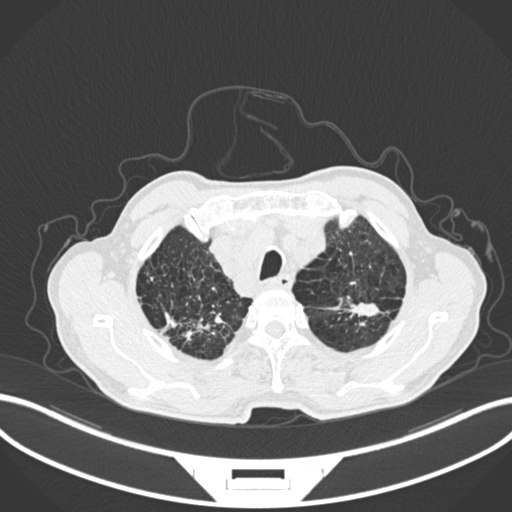
Chest CT, one axial slice. 120 kVp. Lung window (W 1500 / L -600 HU). 512 × 512 image matrix. Patient: male, 74 years. Case-level facts recorded for this patient, not image findings: clinical TNM (as recorded): T2a N1 M0.
Structures marked on this image (bounding box drawn by a radiologist):
- lung tumour (recorded histology: adenocarcinoma): bounding box <345,295,381,321> (left, top, right, bottom; pixels)